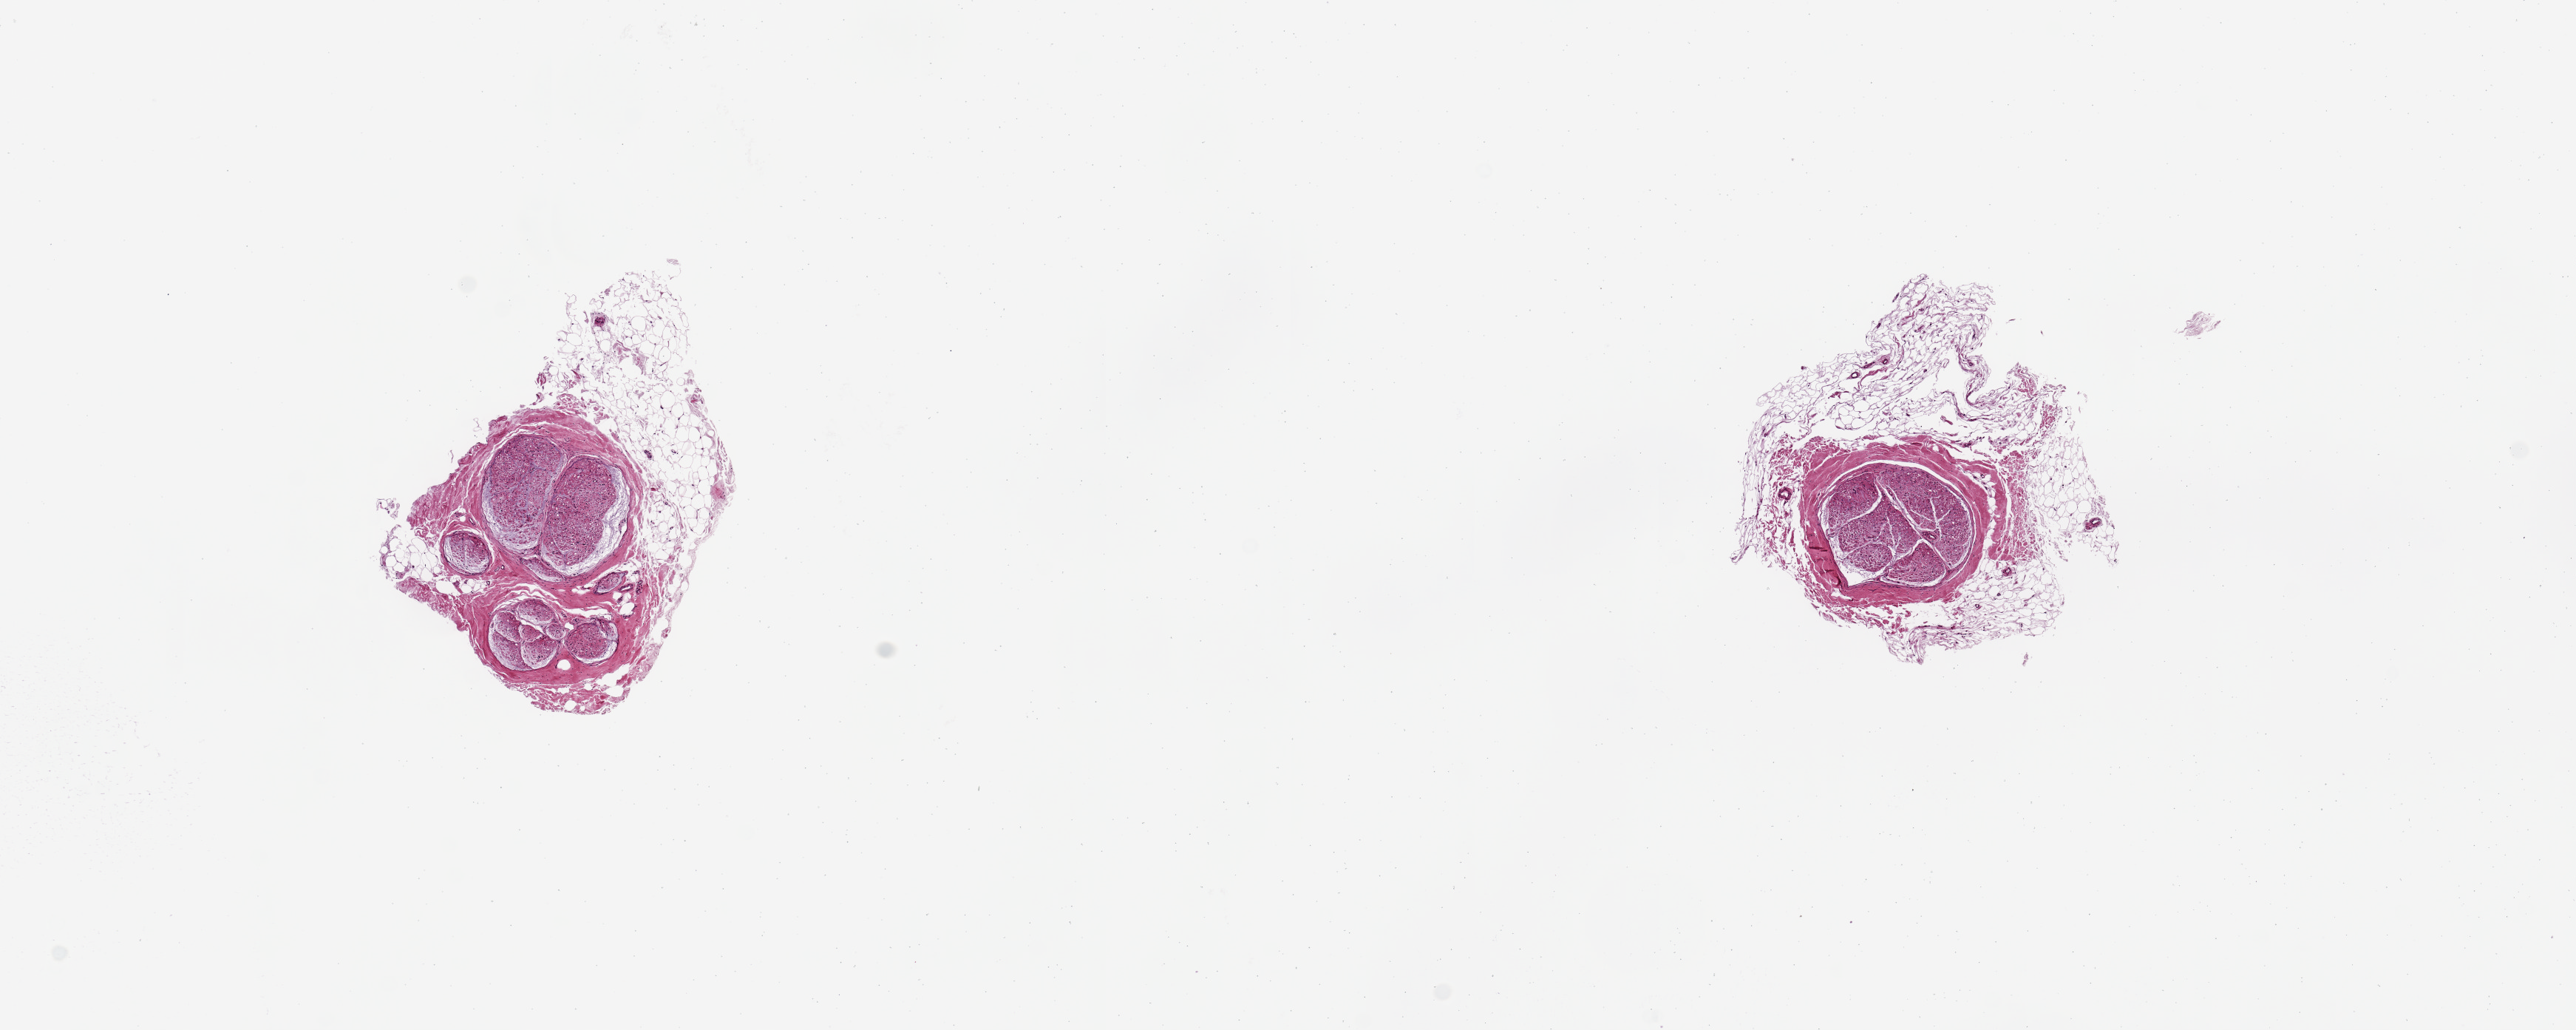
H&E whole-slide image, low-resolution overview of the scanned area, about 13.8 x 5.5 mm (from a 20x scan), PAXgene-fixed, paraffin-embedded tissue, section of tibial nerve (target tissue), donor tissue sample. Donor sex: female.
Reviewer comment on this tissue sample: 2 ~1-1.5mm d. sections. ~40-50% both specimens are rinds of adipose tissue.